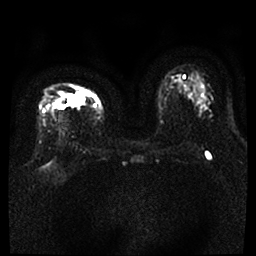
Breast MRI, one axial slice. Slice 24 of 46 in the series (ordered by position). Diffusion-weighted series; image 2 of 4 stored at this slice position (different b-values; order by instance number). 1.5 T. 4 mm slice thickness. 256 × 256 image matrix. Female patient.
Outlined on this slice (manually delineated by an expert):
- tumour on diffusion-weighted imaging: bounding box <54,92,84,109> (left, top, right, bottom; pixels)